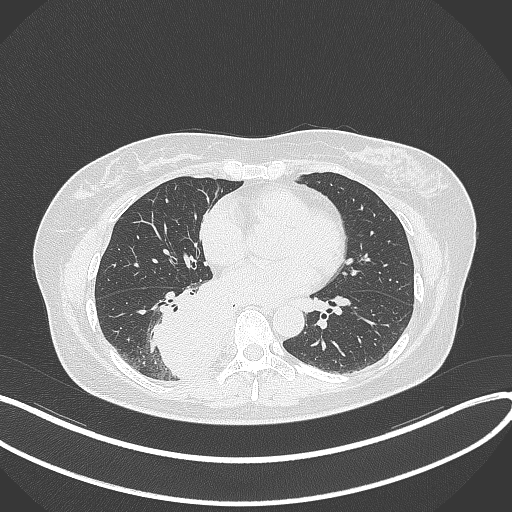
Chest CT, one axial slice; position 157 of 331 along the scan axis; 120 kVp; lung window (W 1500 / L -600 HU); 1 mm slice thickness; 512 × 512 image matrix. Female patient, age 54 years. From the clinical record (not read from this slice): clinical TNM (as recorded): T4 N0 M0.
Annotated regions visible in this slice (rectangle marked by the reading radiologist):
- lung tumour (recorded histology: adenocarcinoma): bounding box (x1, y1, x2, y2) in pixels: (144, 282, 225, 380)